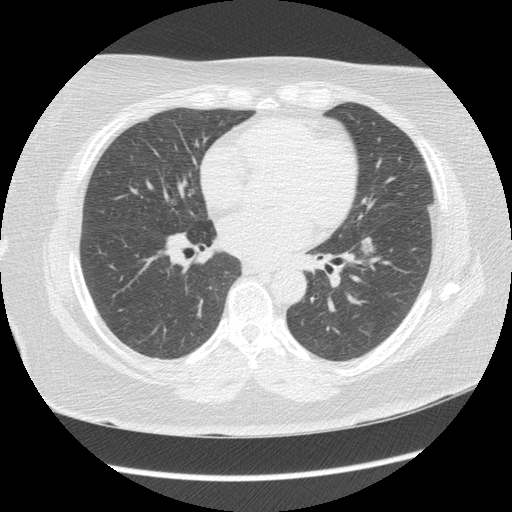
Low-dose screening chest CT, one axial slice. Reconstruction kernel STANDARD. 120 kVp. Lung window (W 1500 / L -600 HU). 2.5 mm slice thickness. 512 × 512 image matrix, field of view 360 × 360 mm.
Structures marked on this image (manually delineated by an expert):
- lesion 1 (tumor, lower lobe of left lung): box from (x=359, y=237) to (x=375, y=256) px